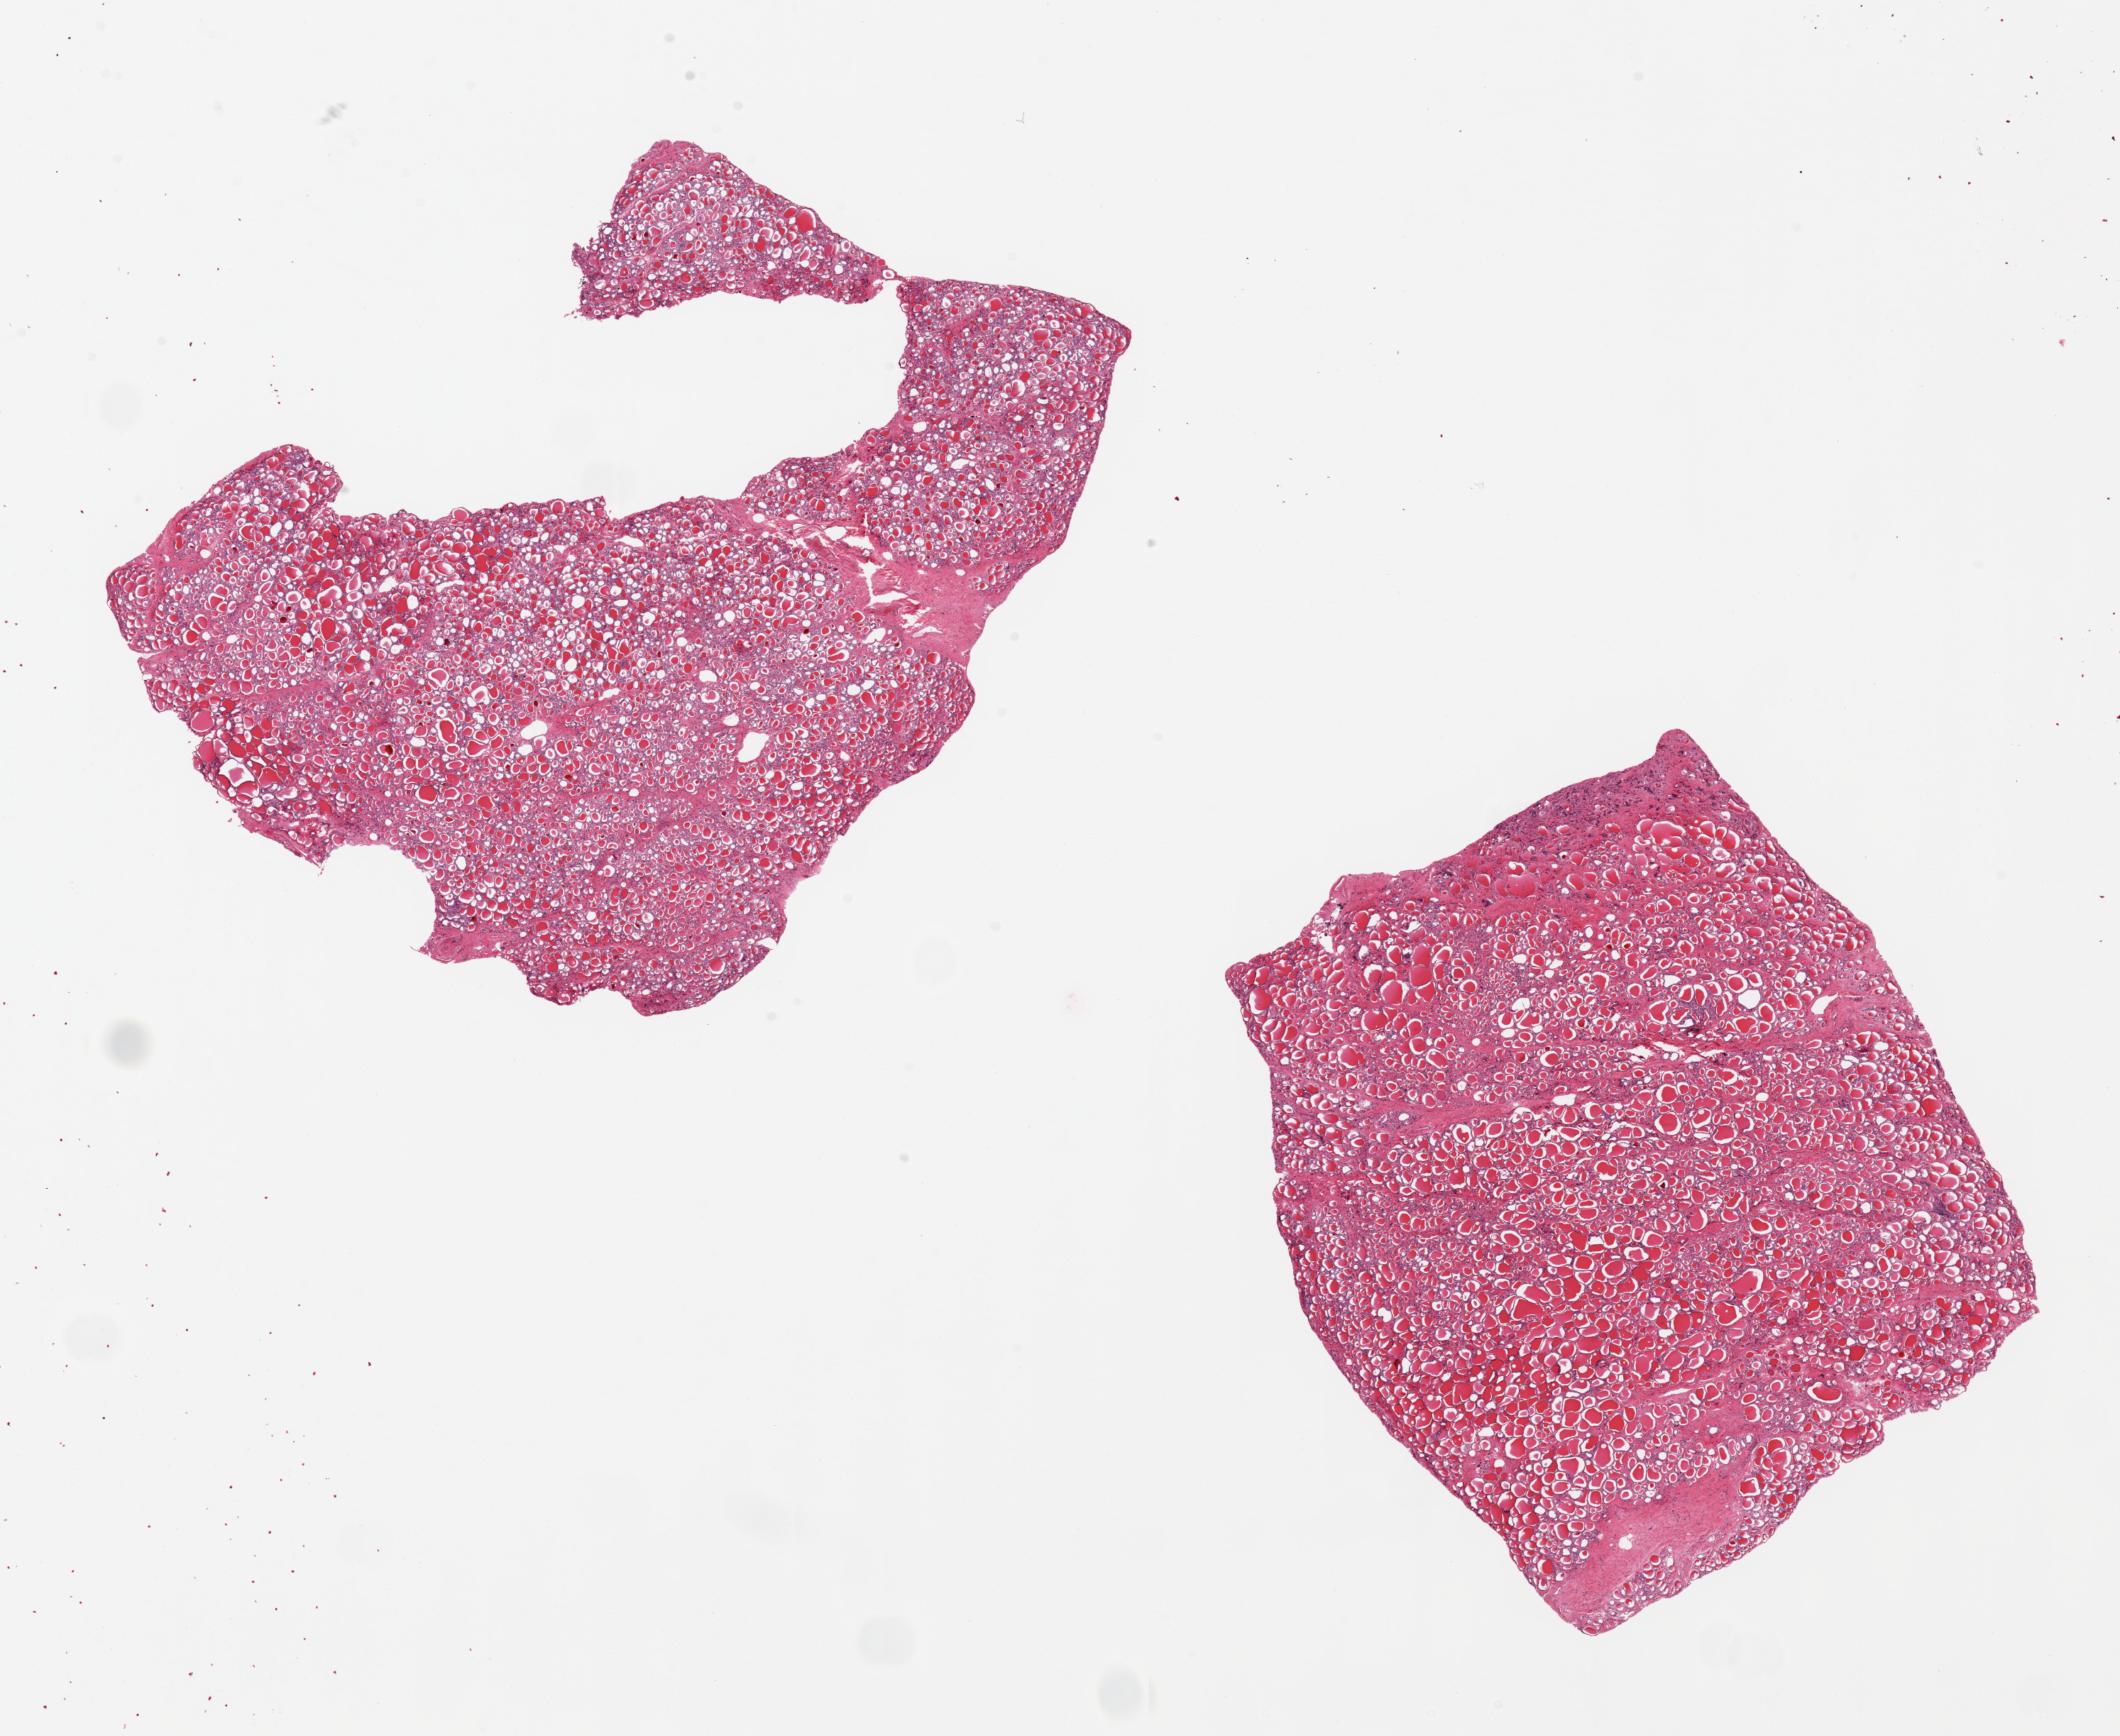
Whole-slide image, hematoxylin and eosin (H&E) stain — shown as a low-resolution overview of the whole scanned area (about 23.6 x 19.3 mm, acquisition: 20x scan), PAXgene-fixed, paraffin-embedded tissue, sampled site (target tissue): thyroid, tissue donor sample.
Pathologist's review note for this sample: 2 pieces, 9x8 & 10x8mm. Good uniform parenchyma.